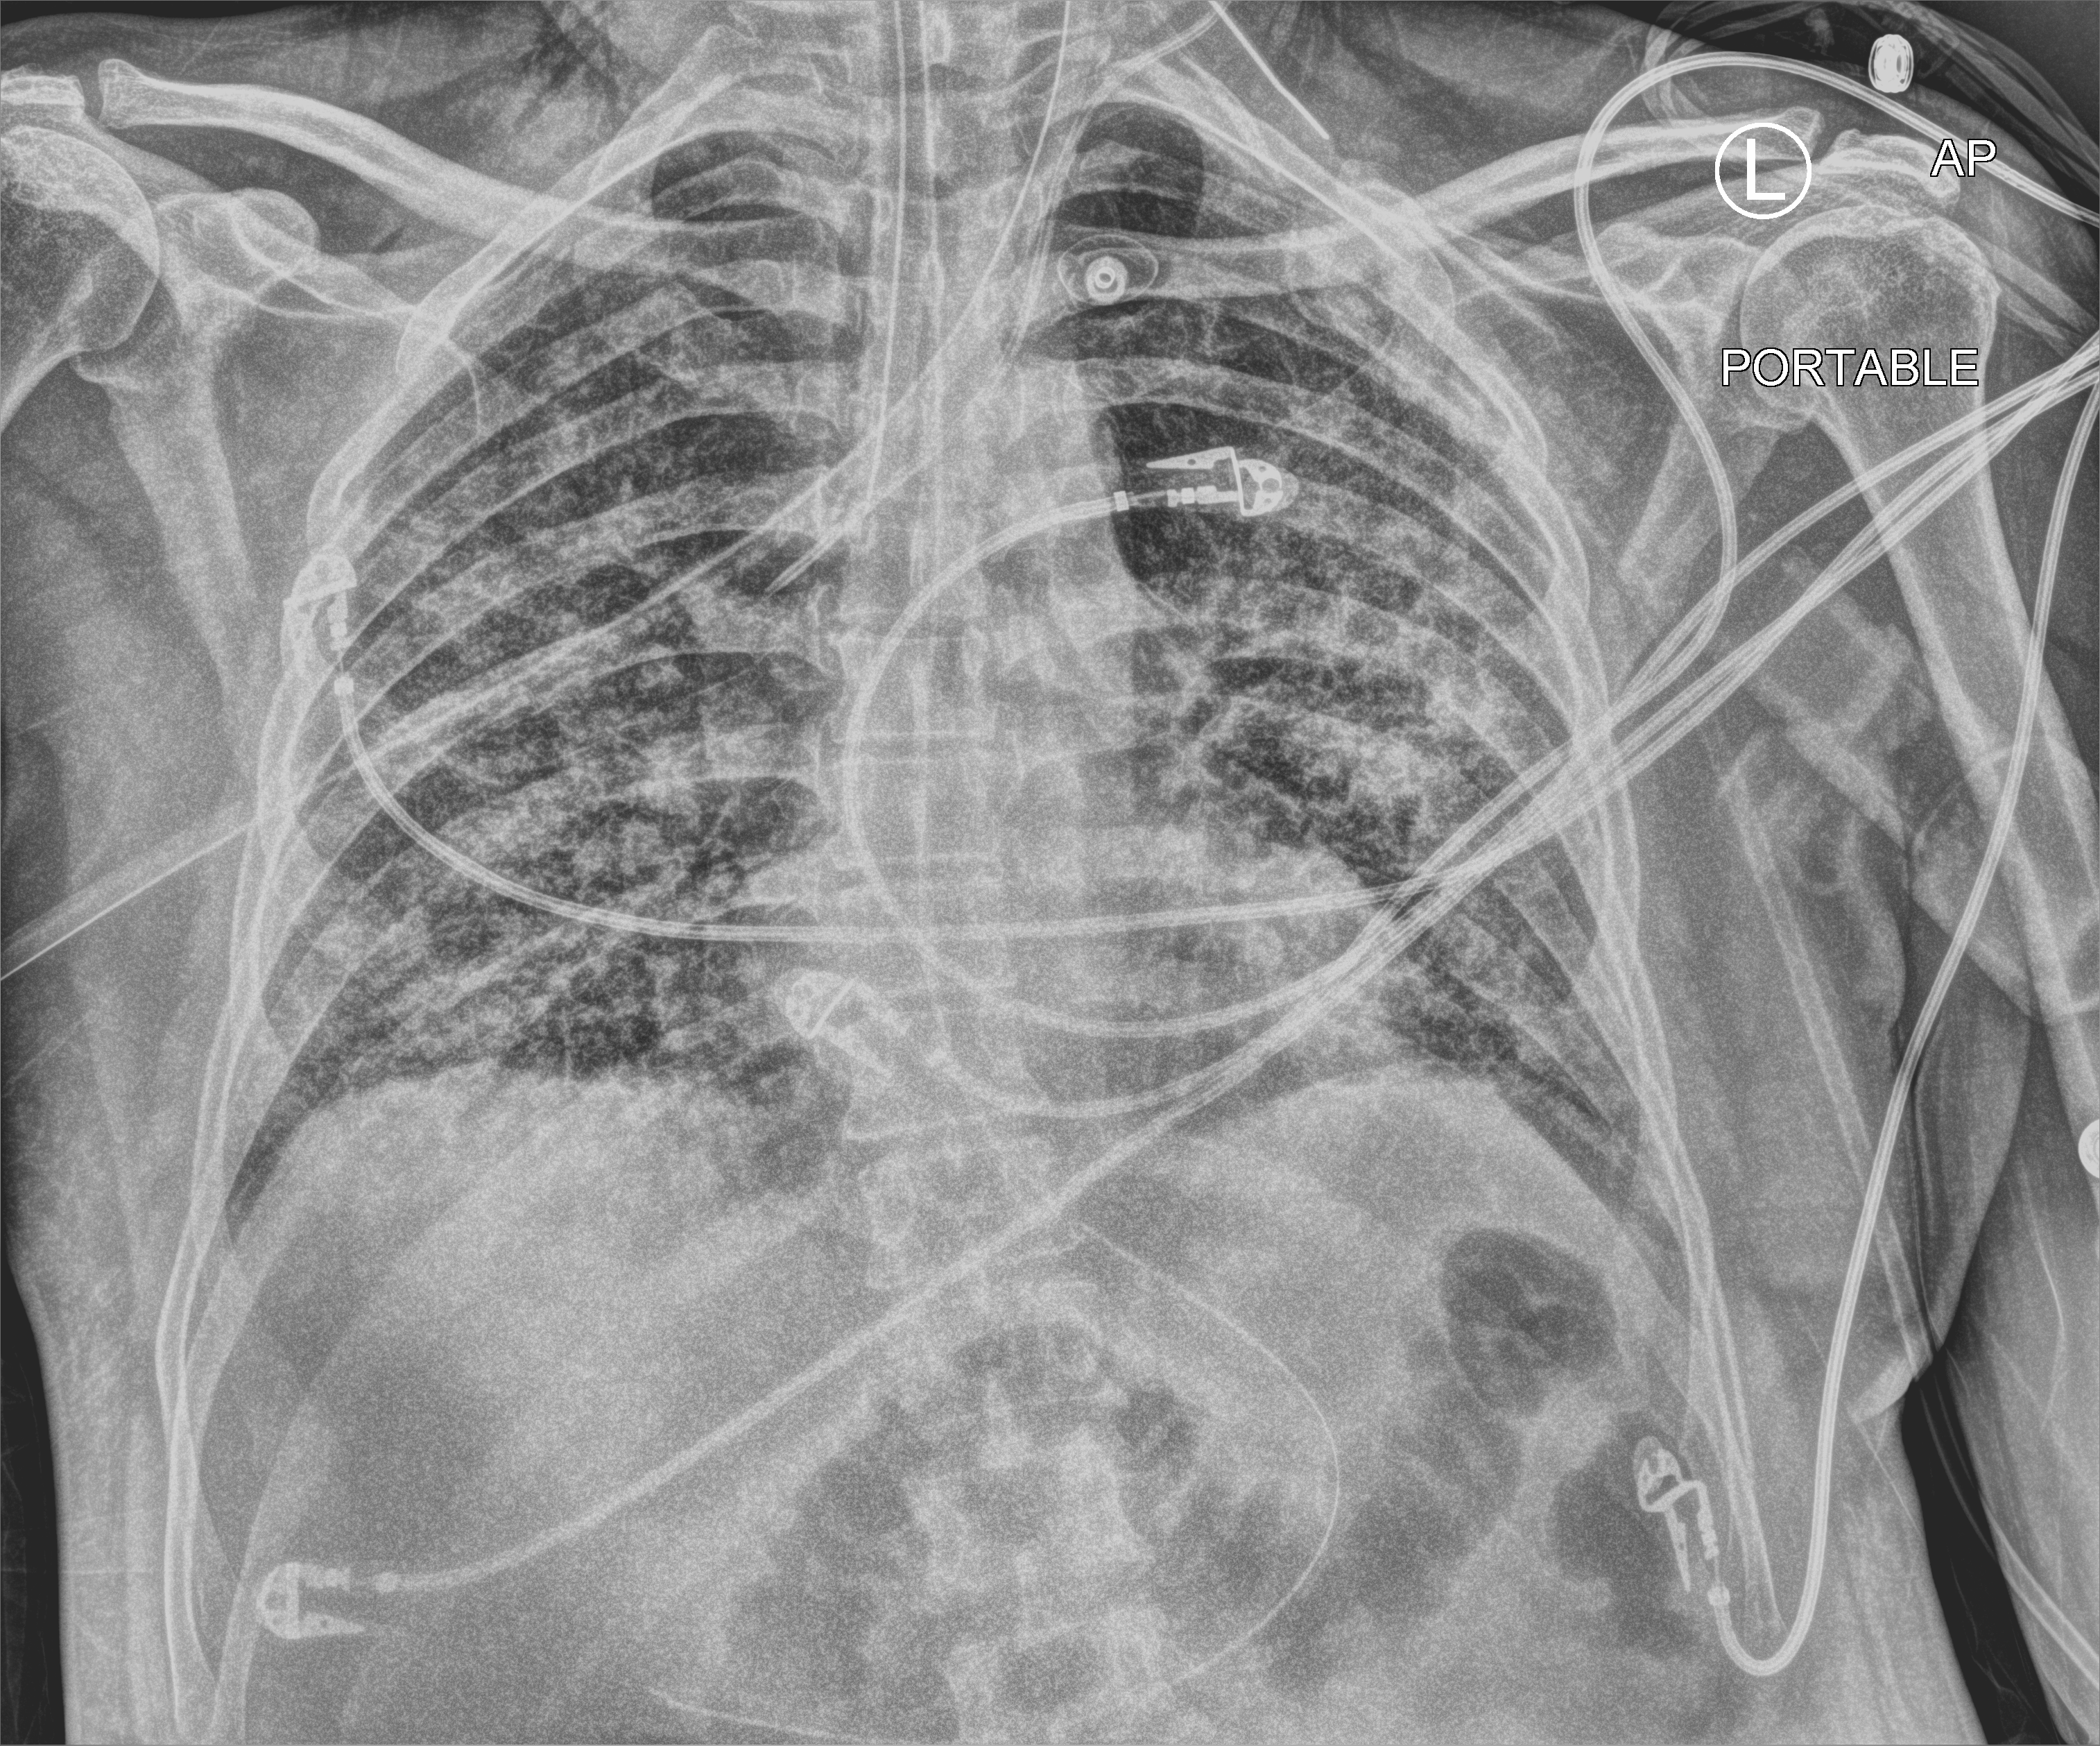
Portable chest radiograph; anteroposterior (AP) projection. Patient hospitalised with COVID-19; male, aged 60–74 years.
Hospital-stay facts (about this admission, not read from this image; timing relative to this image not recorded): mechanically ventilated during this hospital stay: yes.